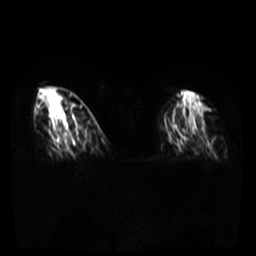
Breast MRI, one axial slice; slice 14 of 36 in the series (ordered by position); diffusion-weighted series; image 2 of 4 stored at this slice position (different b-values; order by instance number); 3 T; 256 × 256 image matrix. Female patient.
Annotated regions visible in this slice (outlined manually by an expert reader):
- tumour on diffusion-weighted imaging: bounding box [x1, y1, x2, y2] px = [60, 130, 63, 136]